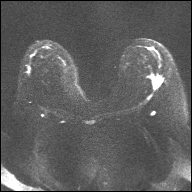
Breast MRI, one axial slice. Position 18 of 32 along the scan axis. Diffusion-weighted series; image 2 of 4 stored at this slice position (different b-values; order by instance number). 1.5 T. 192 × 192 image matrix, field of view 360 × 360 mm. Female patient.
Outlined on this slice (expert manual segmentation):
- tumour on diffusion-weighted imaging: bounding box [x1, y1, x2, y2] px = [154, 77, 160, 87]